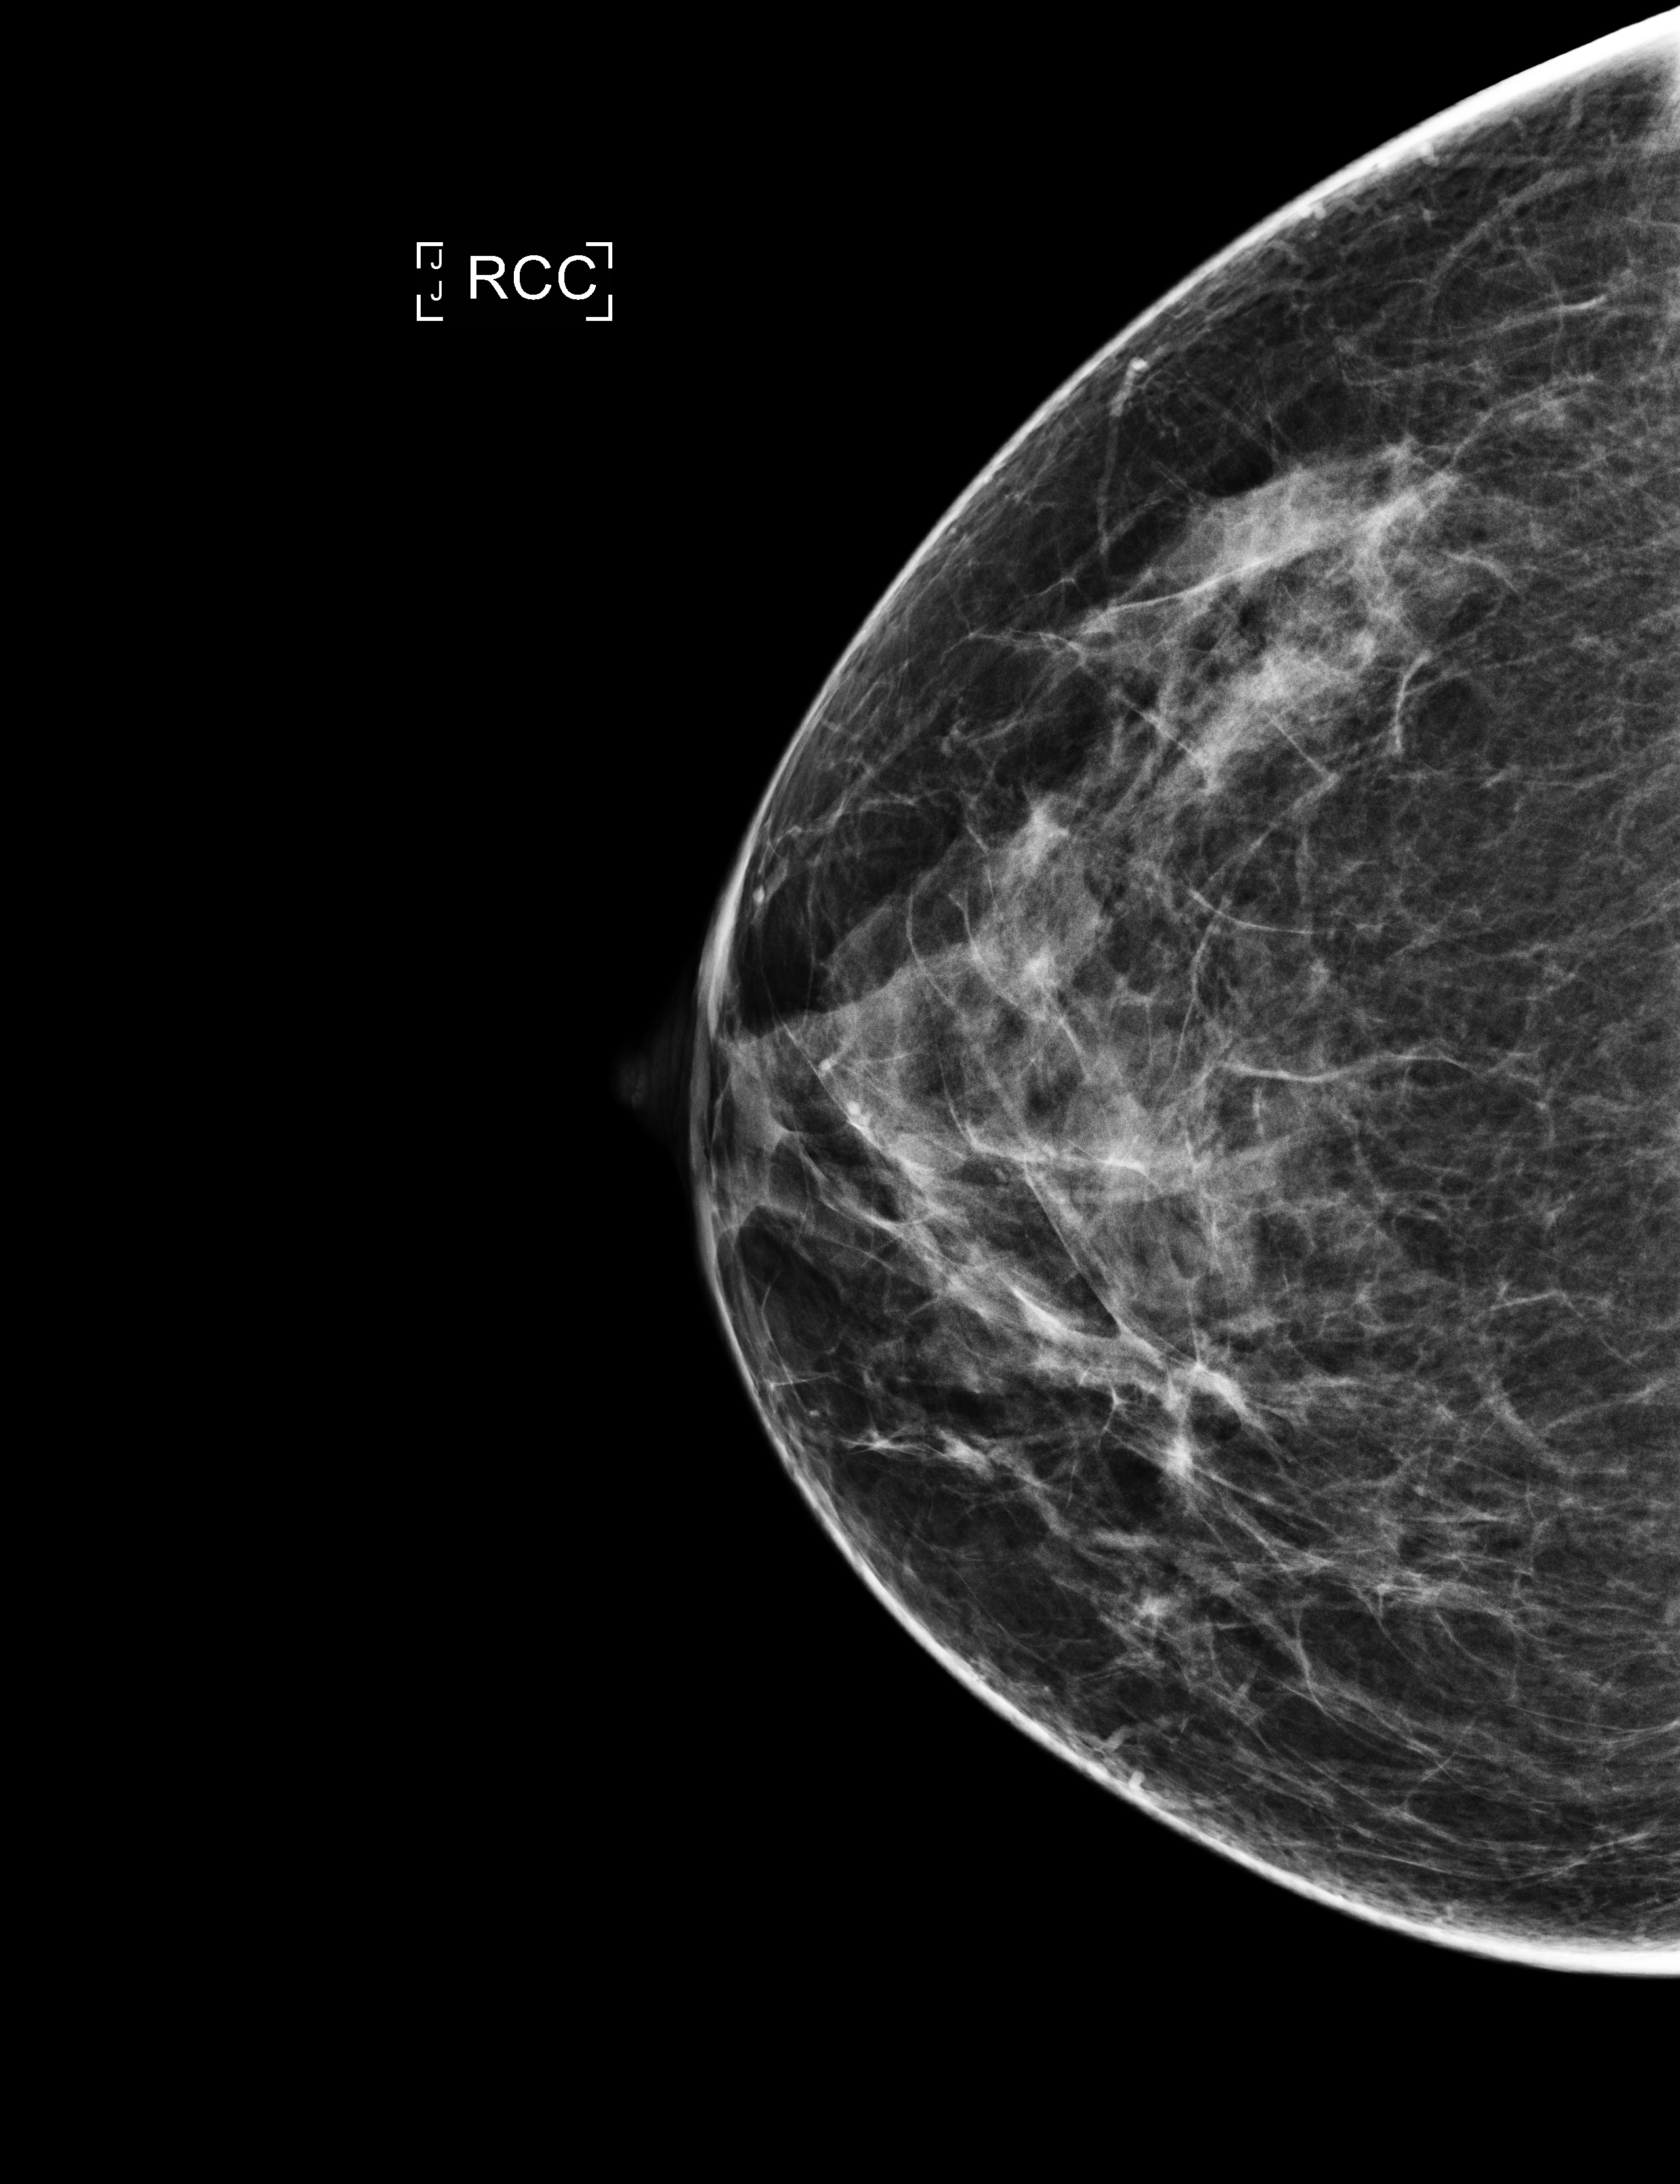
Full-field digital mammogram (FFDM), right breast, cranio-caudal projection, annual screening mammography examination, compressed breast thickness 68 mm. Female patient, age 53 years.
Final BI-RADS assessment for this screening round (tomosynthesis exam, both breasts): category 1.